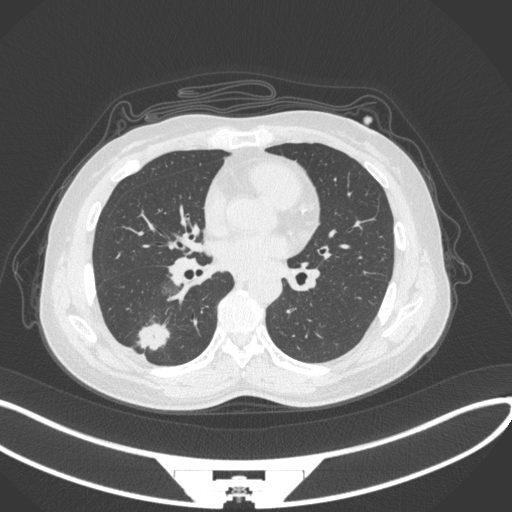
Chest CT, one axial slice; slice 141 of 352 in the series (ordered by position); lung window (W 1500 / L -600 HU); 512 × 512 image matrix, field of view 400 × 400 mm. Patient: female, 55 years. From the clinical record (not read from this slice): clinical TNM (as recorded): T1c N1 M0.
Outlined on this slice (bounding box drawn by a radiologist):
- lung tumour (recorded histology: adenocarcinoma): box from (x=134, y=322) to (x=177, y=358) px